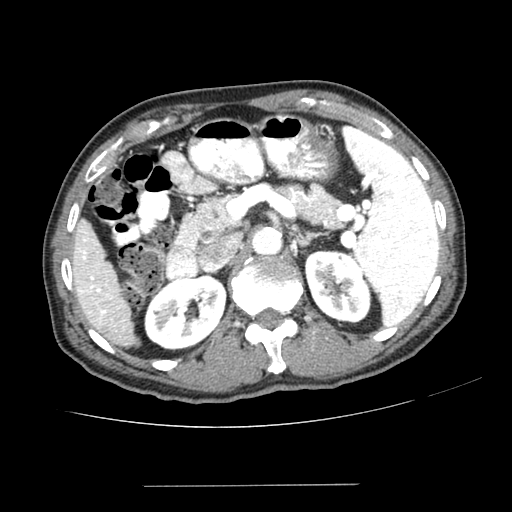
Contrast-enhanced abdominal CT (liver protocol), one axial slice; position 142 of 187 along the scan axis; reconstruction kernel SOFT; one of 2 acquisitions stored at this slice position; soft-tissue window (W 400 / L 40 HU); 2.5 mm slice thickness; 512 × 512 image matrix, field of view 360 × 360 mm. From the clinical record (not read from this slice): diagnosis: hepatocellular carcinoma (patient treated with transarterial chemoembolisation; whether this scan precedes or follows treatment is not stated here); TNM stage (as recorded): Stage-I; Child-Pugh class: A; tumour nodularity: uninodular; tumour size: 1.6 cm.
Outlined on this slice (semi-automatically segmented with operator editing):
- liver parenchyma outside the tumour (the mass and vessels are separate outlines, so this box may not span the whole liver): bounding box [x1, y1, x2, y2] px = [70, 218, 136, 346]
- liver vessels: [79, 239, 108, 320]